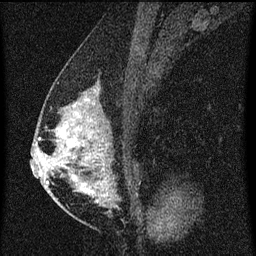
Breast MRI (dynamic contrast-enhanced), one sagittal slice; position 31 of 60 along the scan axis; dynamic contrast-enhanced series, image 2 of 3 at this slice position (ordered by acquisition); 1.5 T; TE 4.2 ms, TR 8 ms; 256 × 256 image matrix, field of view 180 × 180 mm. Female patient, age 47 years.
Outlined on this slice (semi-automatically segmented with operator editing):
- analysis volume of interest (the breast-tissue region the enhancement analysis was run in; not a lesion): bounding box (x1, y1, x2, y2) in pixels: (50, 80, 139, 203)
- tumour enhancement mask (voxels above the 70 % enhancement threshold inside the analysis volume of interest): (56, 90, 109, 203)